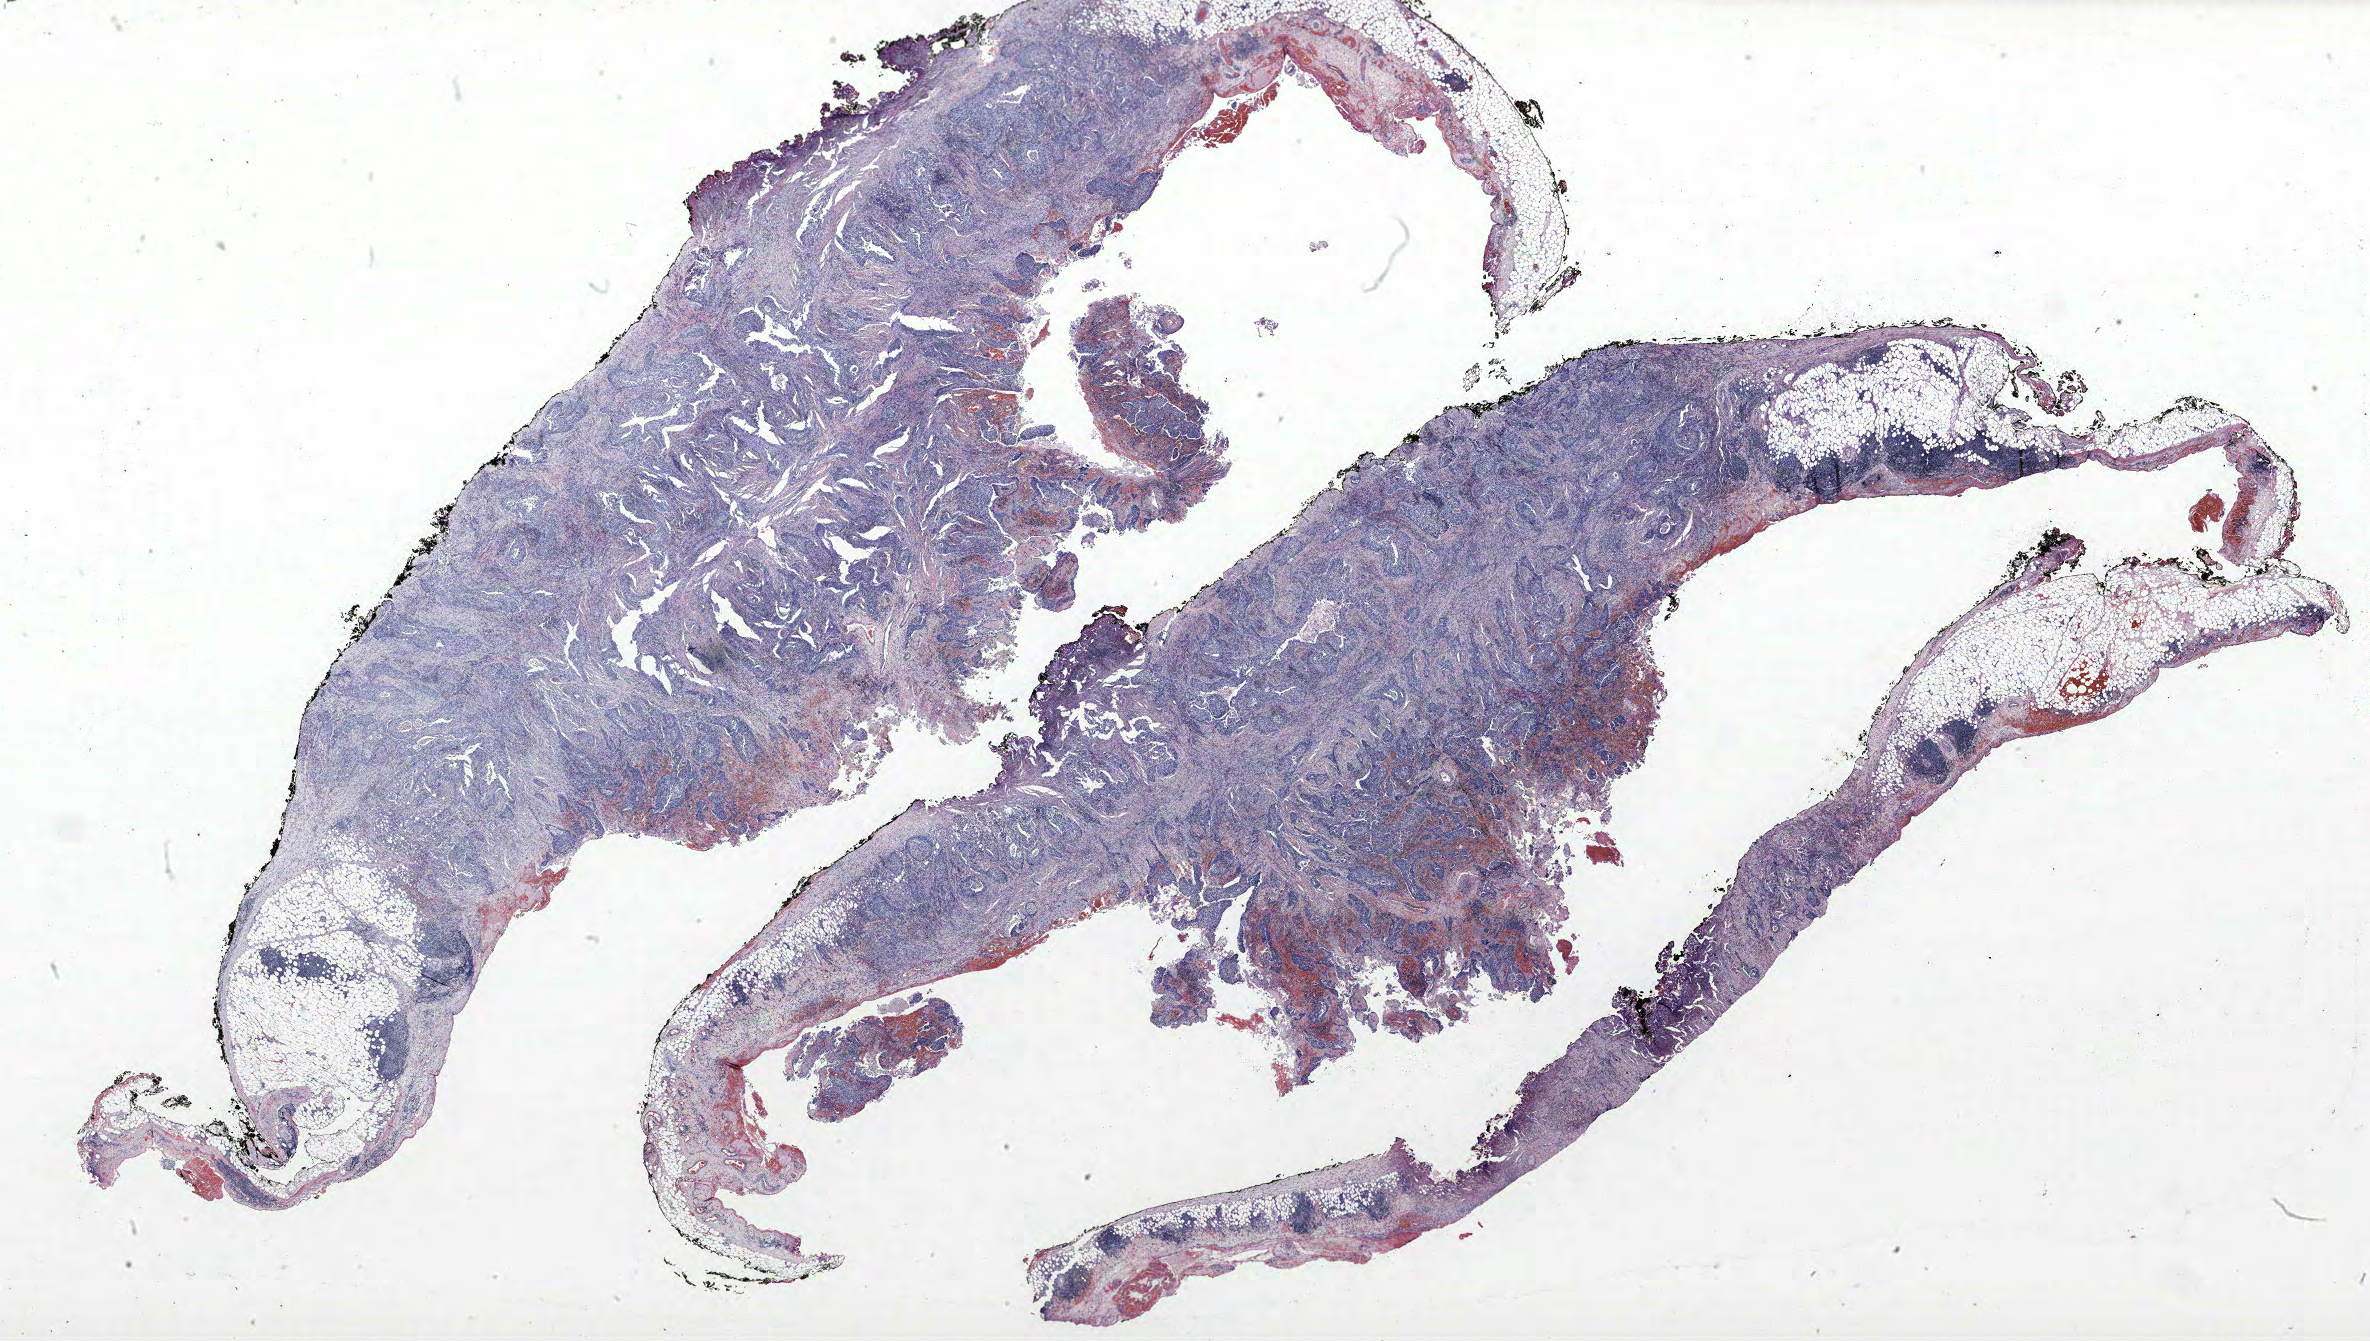
Whole-slide histology image, H&E — low-resolution overview of the scanned area, about 37.9 x 21.5 mm (acquisition: 40x scan); FFPE section; lung. Male patient, aged 64 at enrolment.
Participant's lung-cancer diagnosis: Squamous cell carcinoma, NOS.